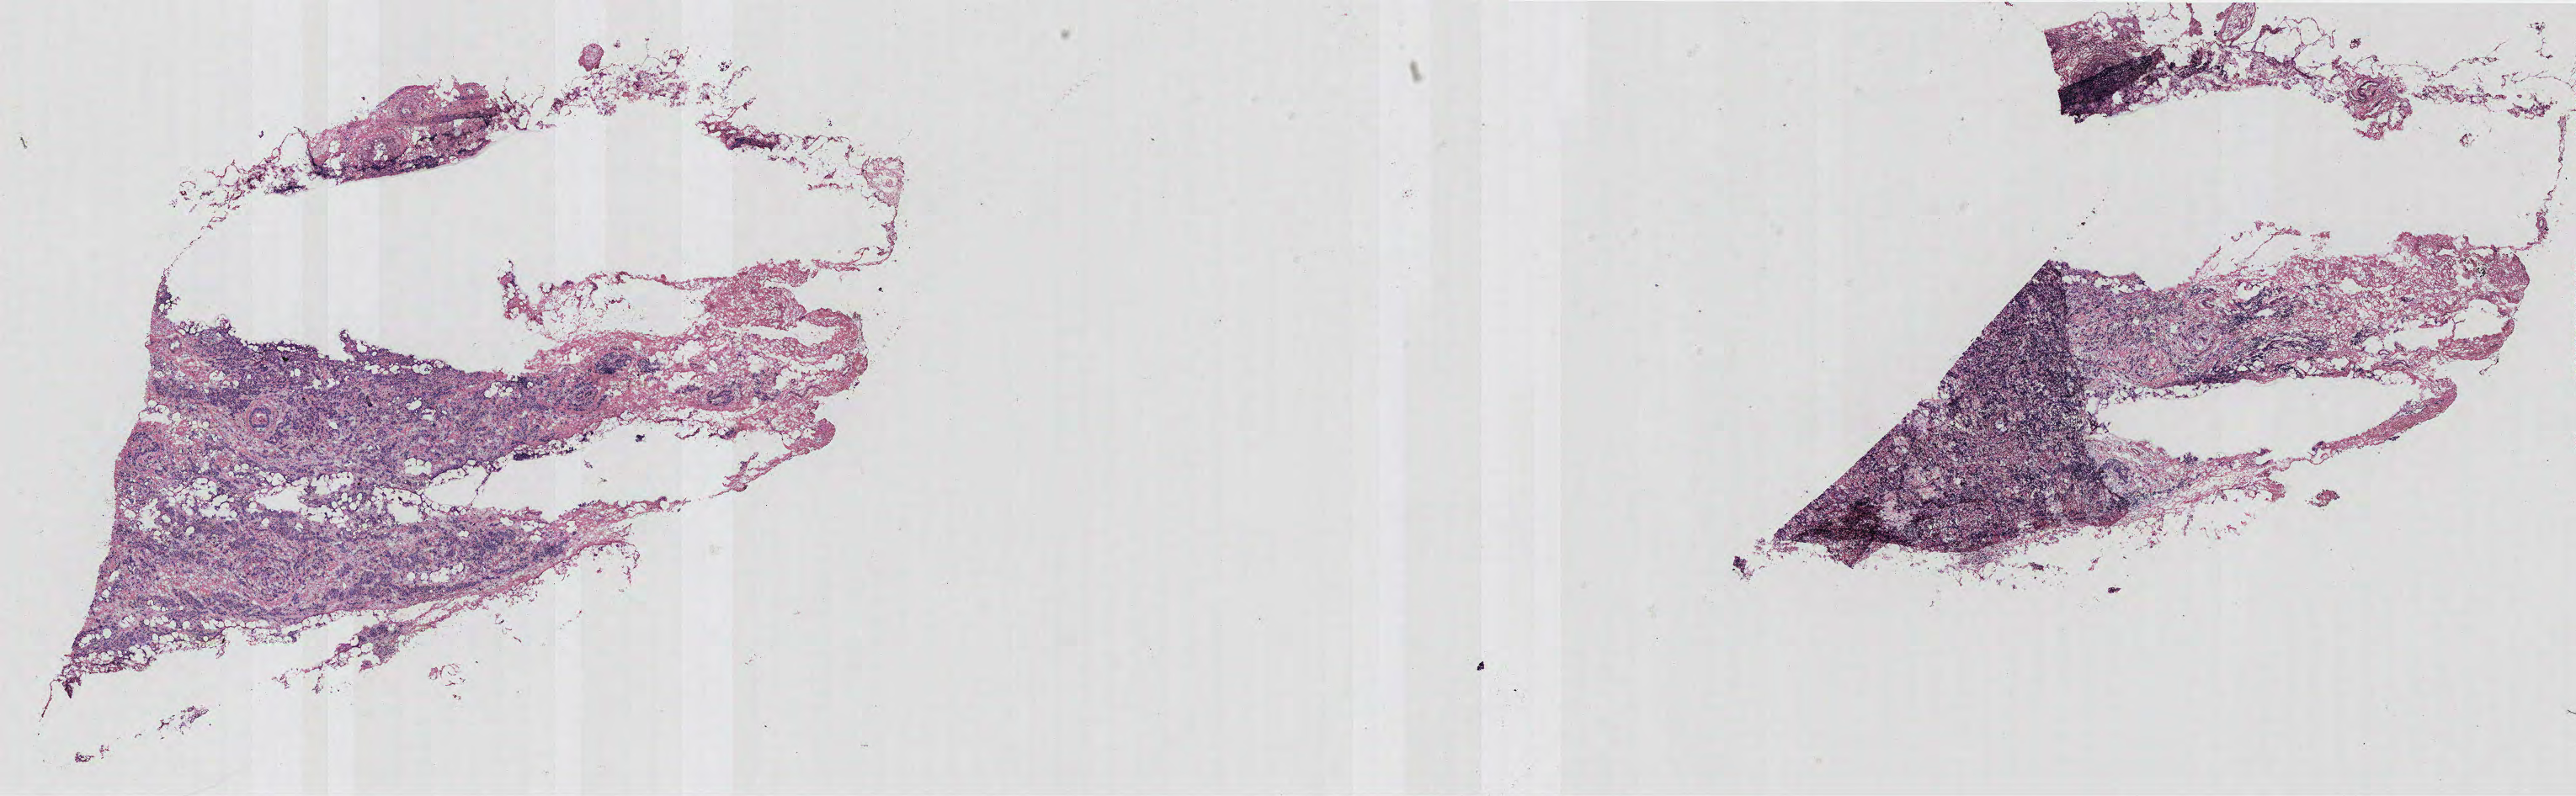
H&E-stained whole-slide image, low-resolution overview of the scanned area, about 24.5 x 7.6 mm (acquisition: 40x scan). Breast, tumour tissue. Patient: female, age 77 years.
AJCC pathologic stage: IIIA. Diagnosis: Infiltrating duct carcinoma, NOS.